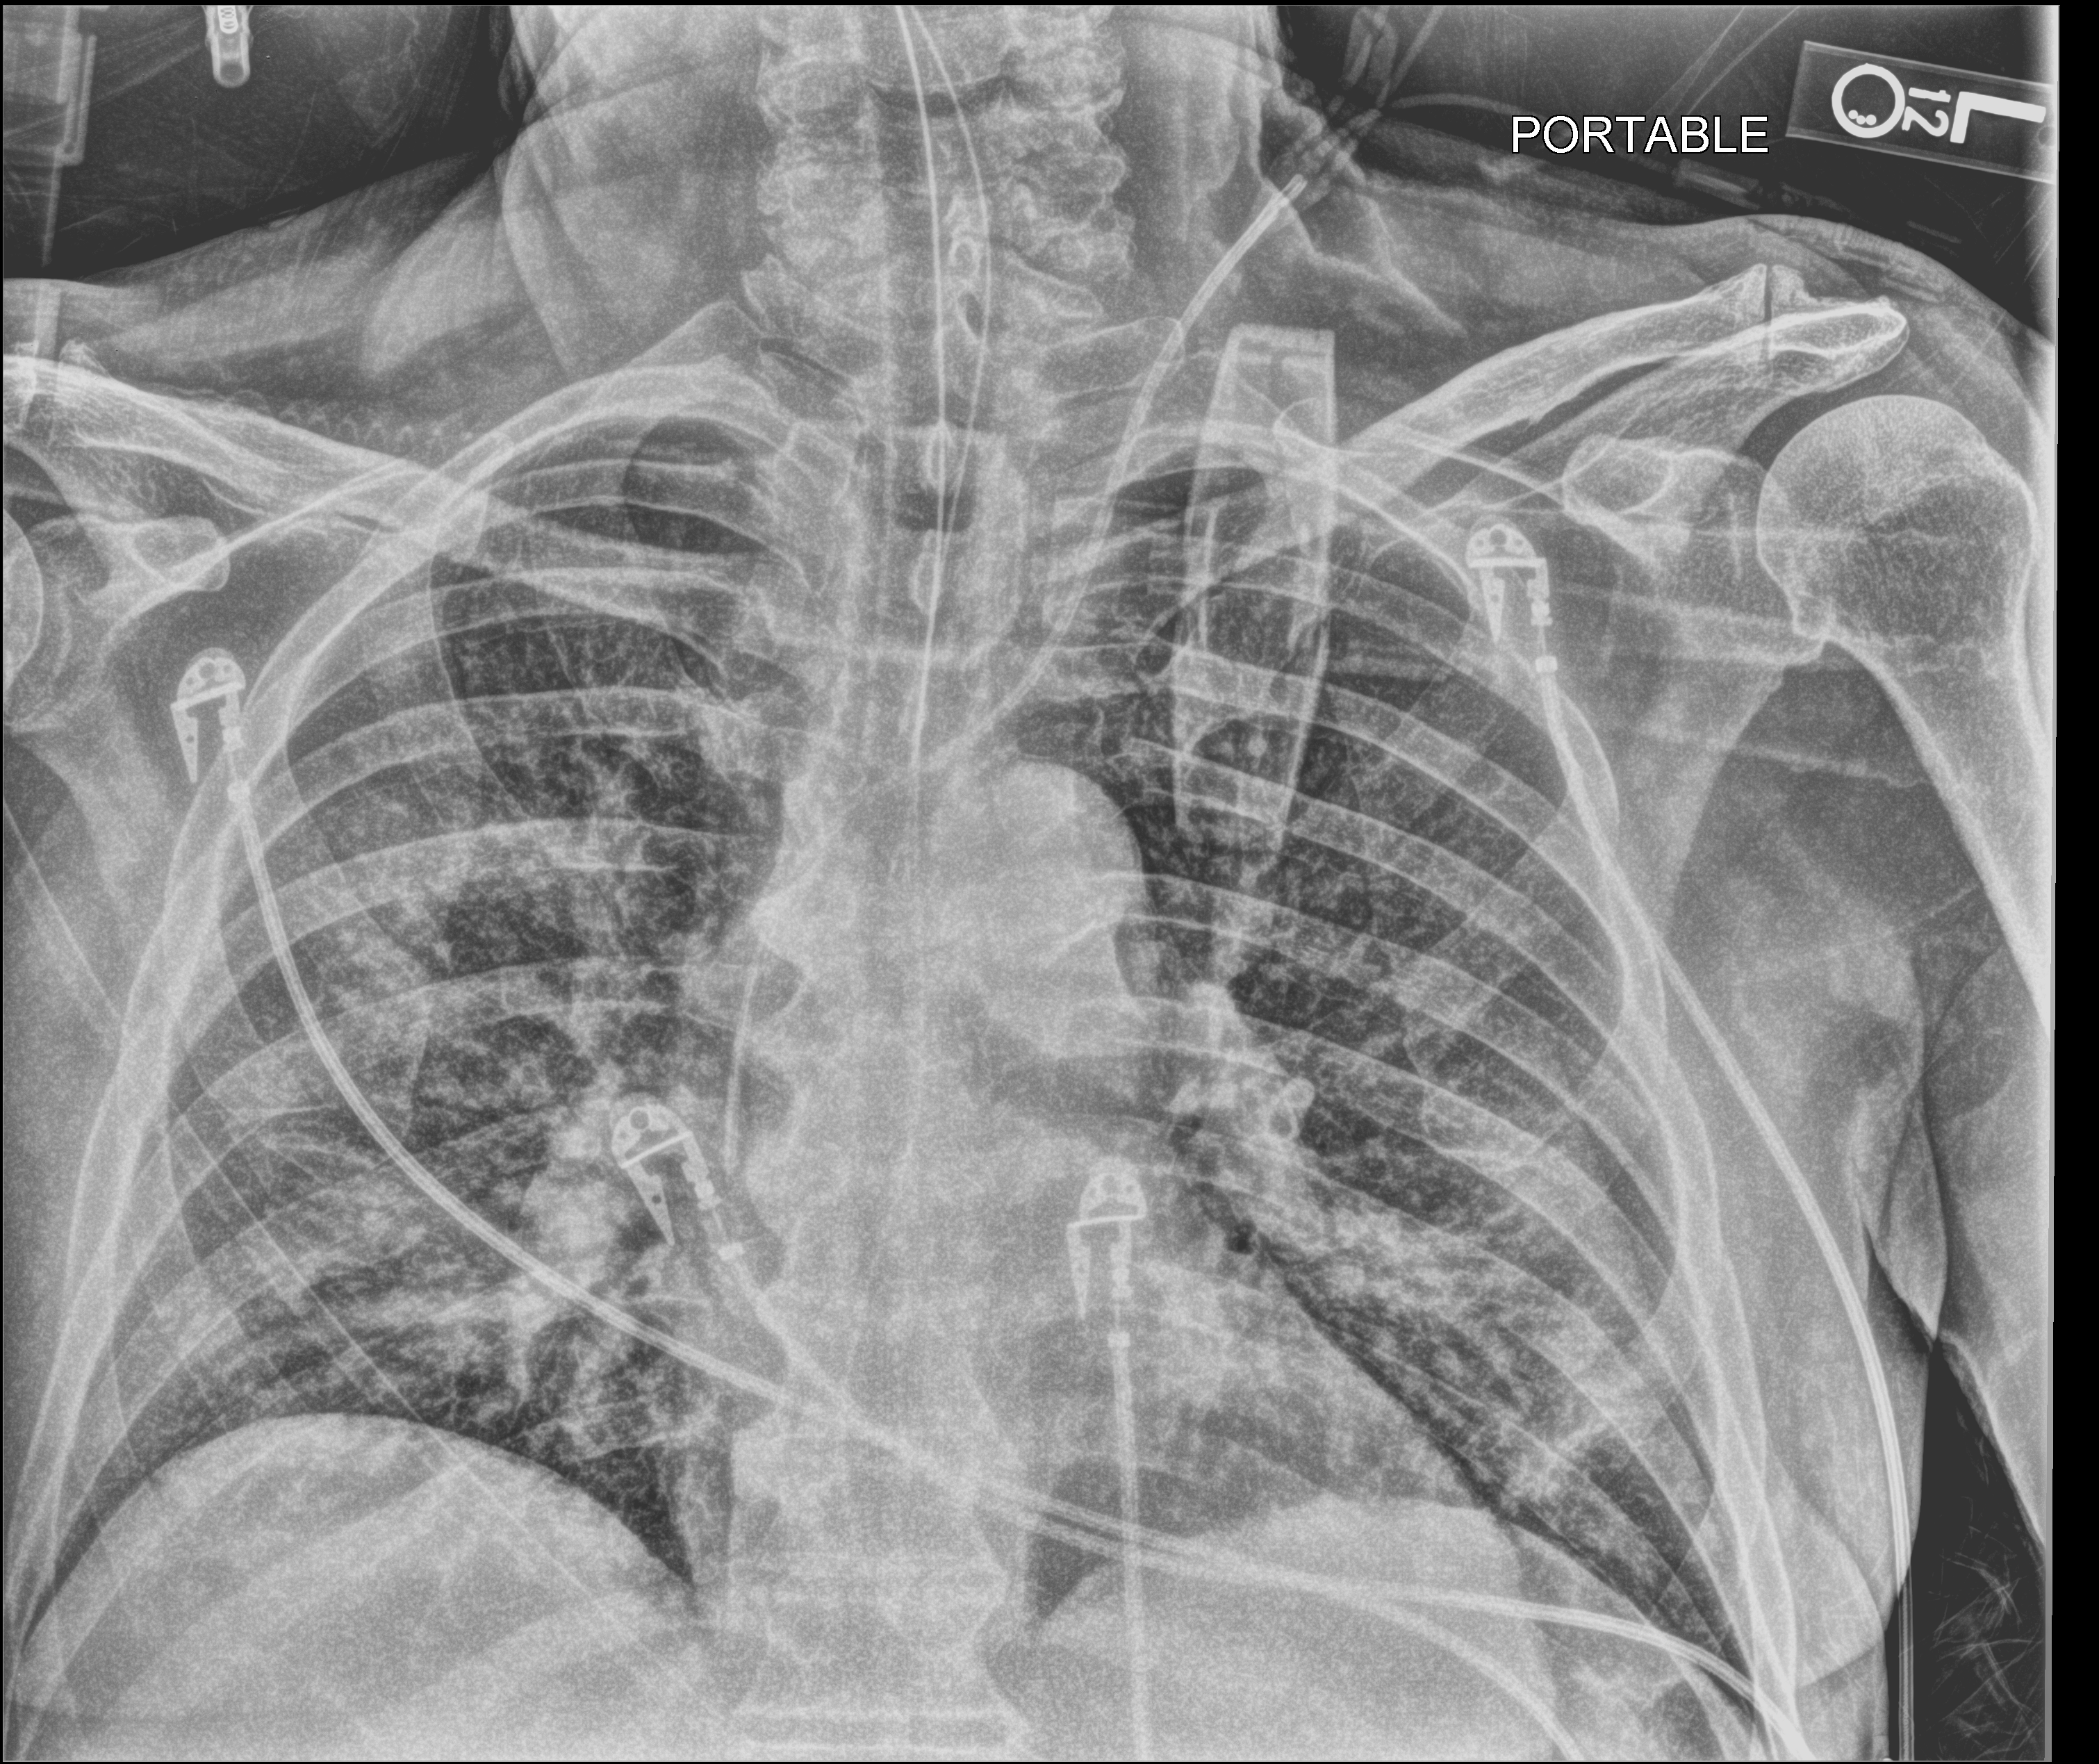
Bedside chest radiograph (computed radiography), anteroposterior (AP) projection. Male patient hospitalised with COVID-19, age 60–74 years.
Hospital-stay facts (about this admission, not read from this image; timing relative to this image not recorded):
- mechanically ventilated during this hospital stay: yes